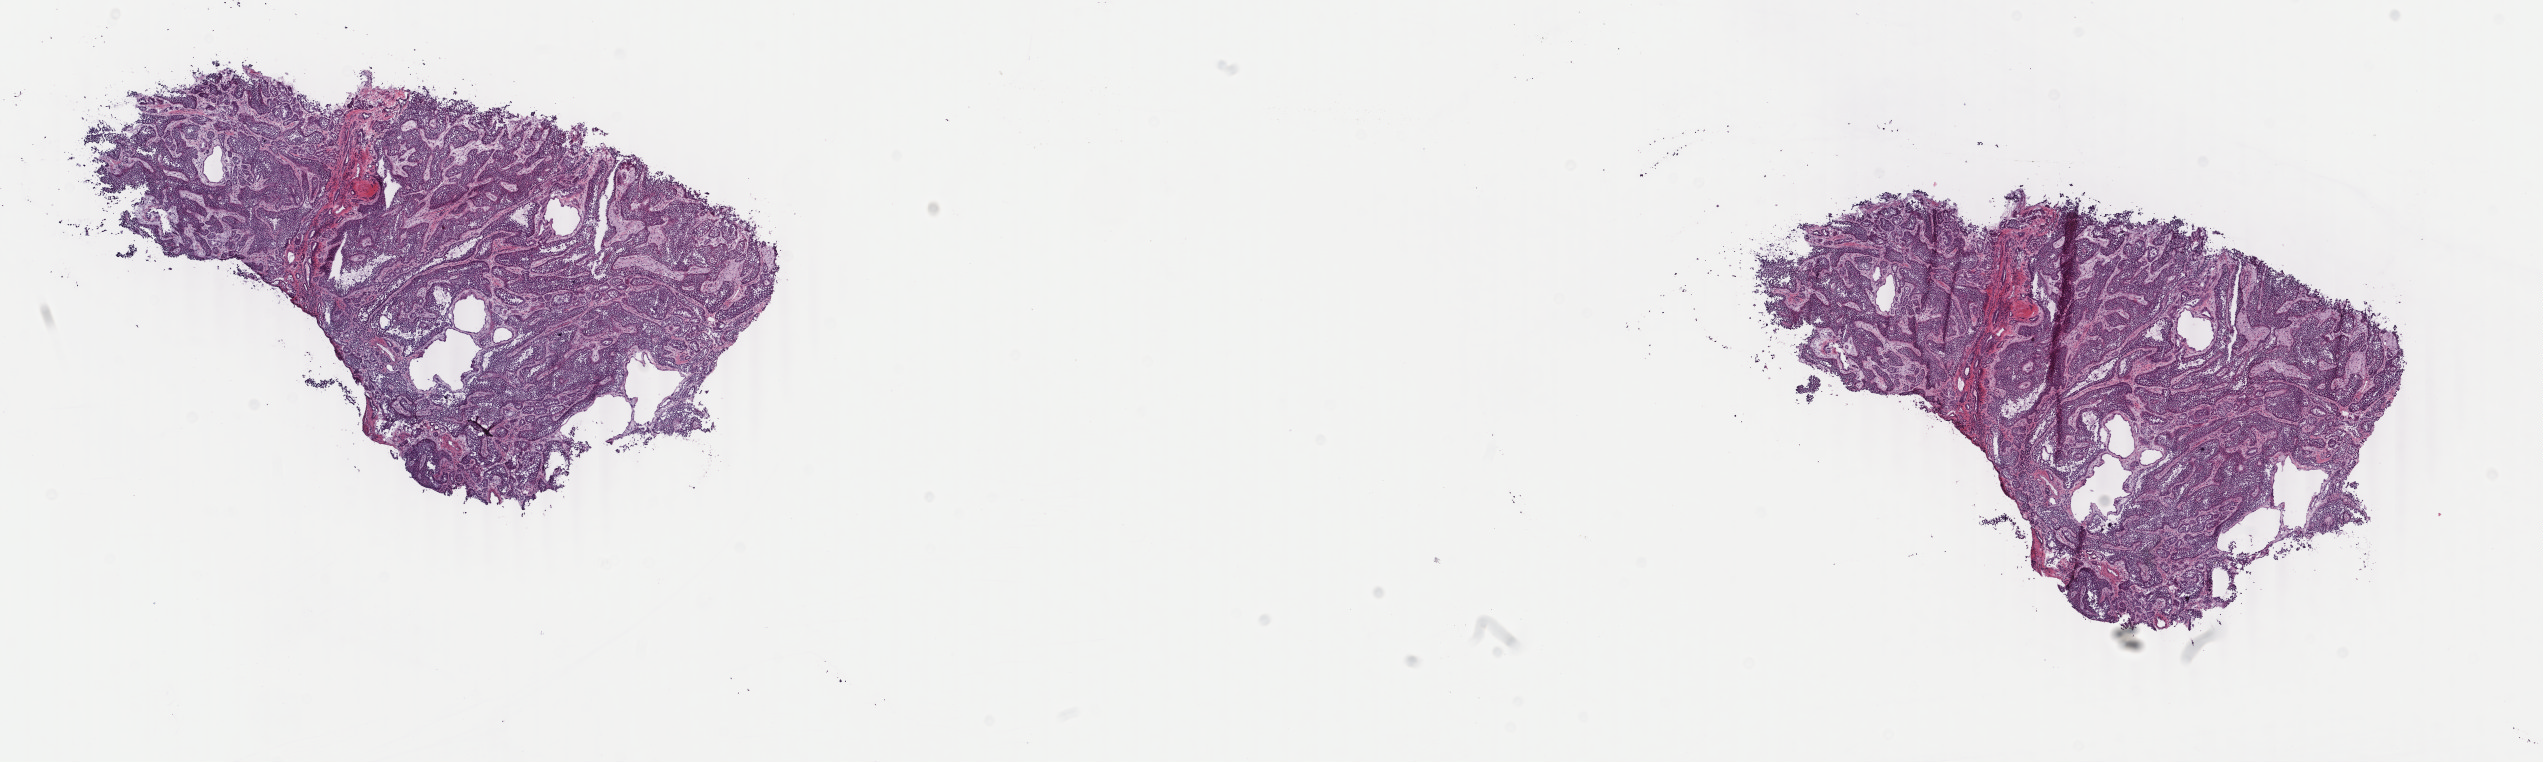
Whole-slide histology image, H&E, low-resolution overview of the scanned area, about 20.2 x 6.1 mm (from a 40x scan), frozen section from the top of the tissue portion, kidney, primary tumour sample. Patient: male, age at initial diagnosis 40 years. Slide review estimates, as recorded: tumour cells 100%, tumour nuclei 75%, normal cells 0%, stromal cells 0%, necrosis 0%. Inflammatory infiltration, as recorded: lymphocyte infiltration 2%, monocyte infiltration 0%, neutrophil infiltration 0%.
• AJCC pathologic stage: I (7th edition)
• diagnosis: Papillary adenocarcinoma, NOS